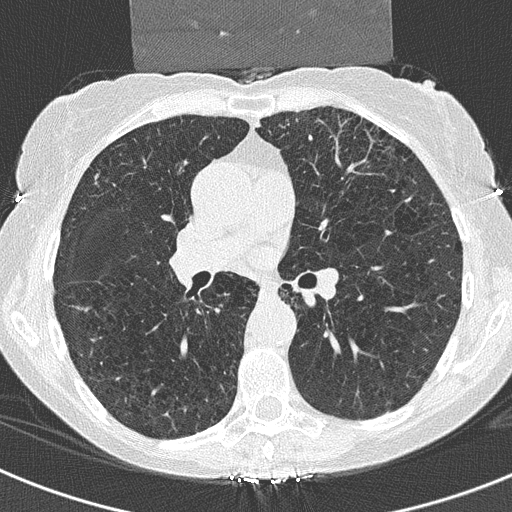
Chest CT (low-dose screening protocol), one axial image. Third annual screen. Lung window (W 1500 / L -600 HU). 2 mm slice thickness. Slice 133 of 325 in the series. Female, age 70 years at enrolment. Current smoker at enrolment.
• Expert reader's lesion annotation, bounding box [x1, y1, x2, y2] px = [70, 158, 111, 196].
• Screening reader's record for this exam (one nodule recorded; not confirmed to be the boxed lesion): non-calcified nodule or mass ≥4 mm, right middle lobe, 5 × 5 mm, spiculated (stellate) margins, ground glass attenuation, pre-existing on the prior screen: no.
• Participant outcome: lung cancer diagnosed 321 days after this screen — adenosquamous carcinoma, right upper lobe, poorly differentiated (G3), stage IA (AJCC 6th edition), 12 mm at pathology.